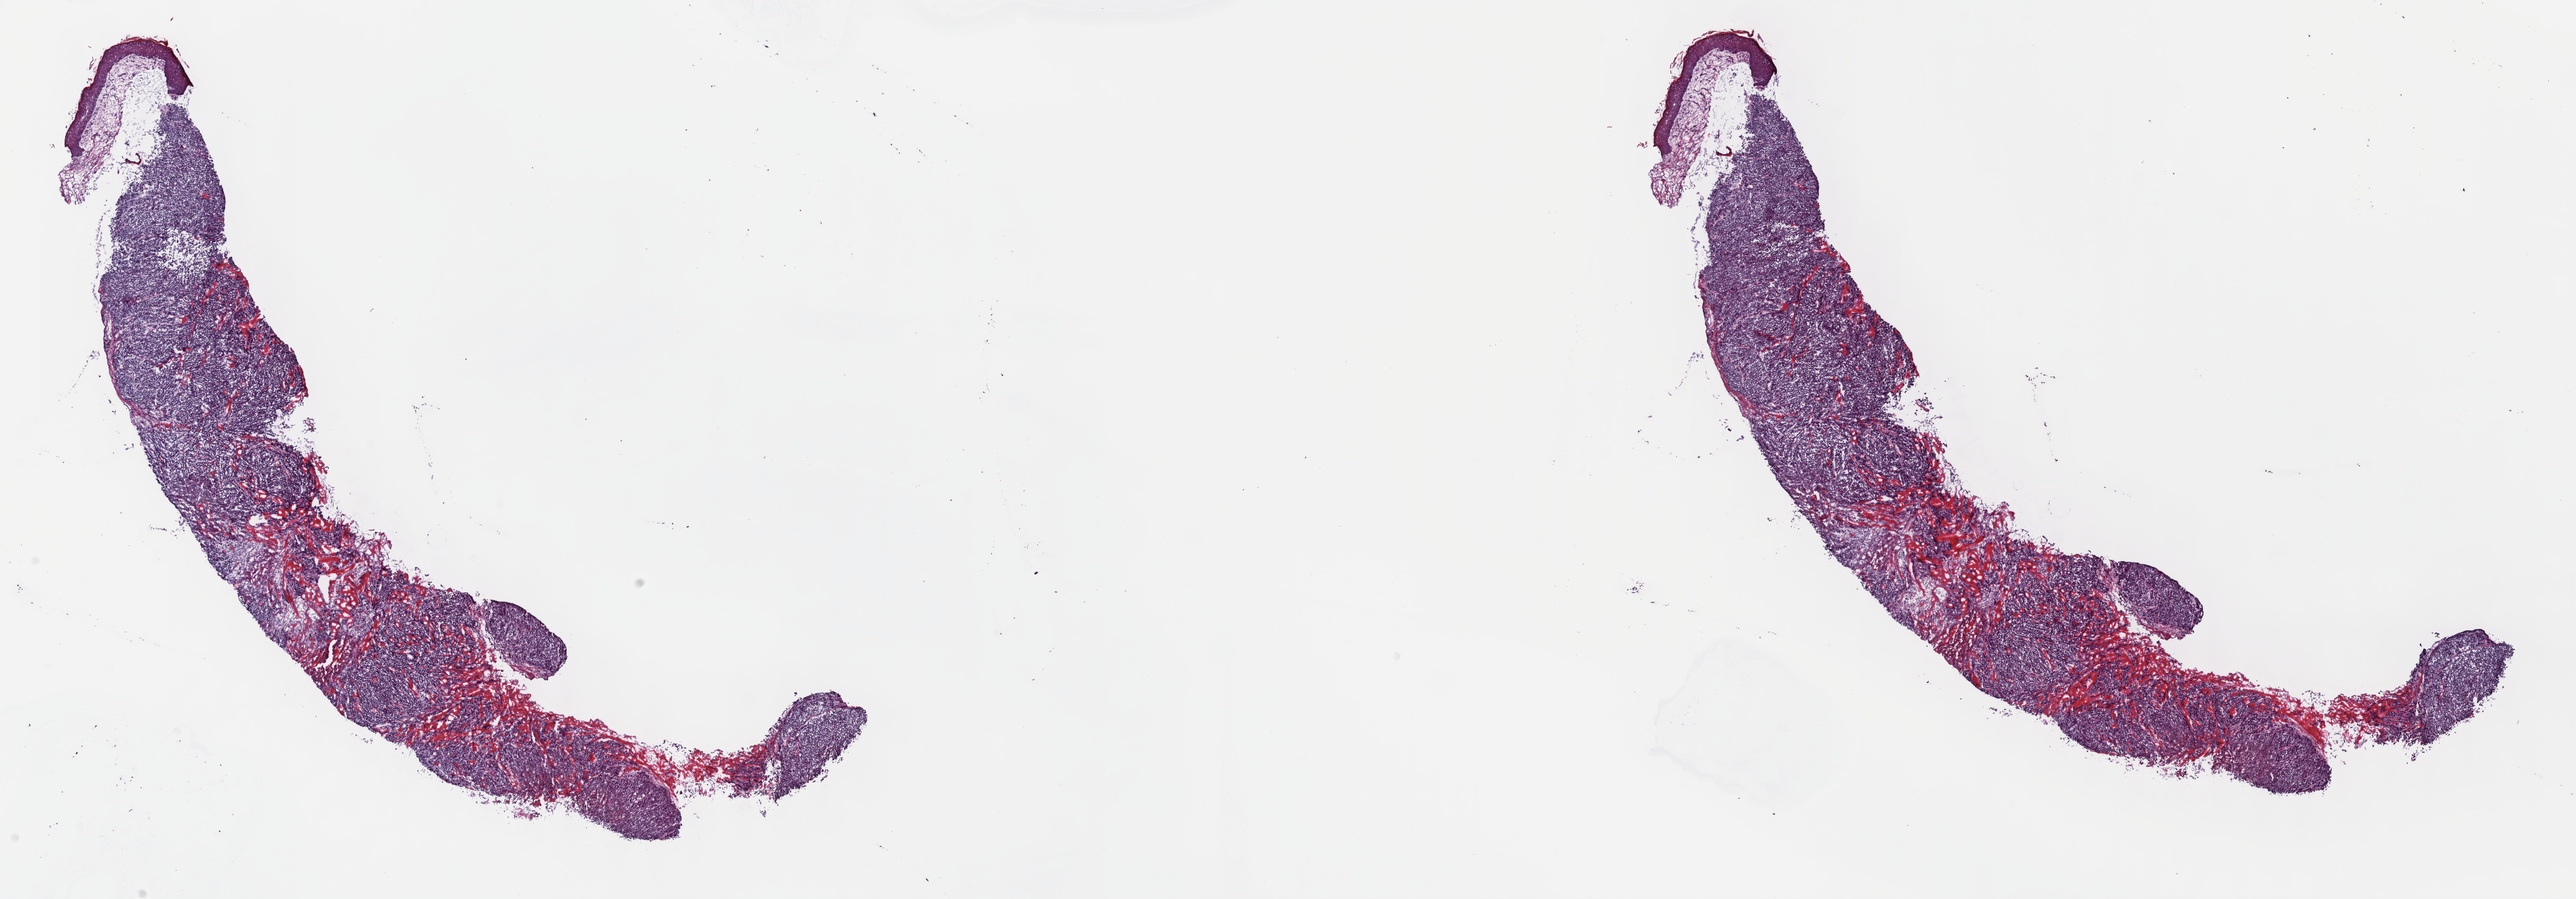
Digitized Hematoxylin and eosin (H&E) stained tissue section (whole slide), a low-resolution overview of the entire scanned area, about 30.7 x 10.7 mm. Frozen section from the top of the tissue portion. Metastatic tumour sample. Patient: male, age at initial diagnosis 71 years. Composition of this section per pathologist review: tumour cells 80%, tumour nuclei 80%, normal cells 3%, stromal cells 17%, necrosis 0%. Infiltration values recorded for this section: lymphocyte infiltration 3%, monocyte infiltration 1%, neutrophil infiltration 2%.
* this section: metastatic tumour tissue
* patient diagnosis: Malignant melanoma, NOS